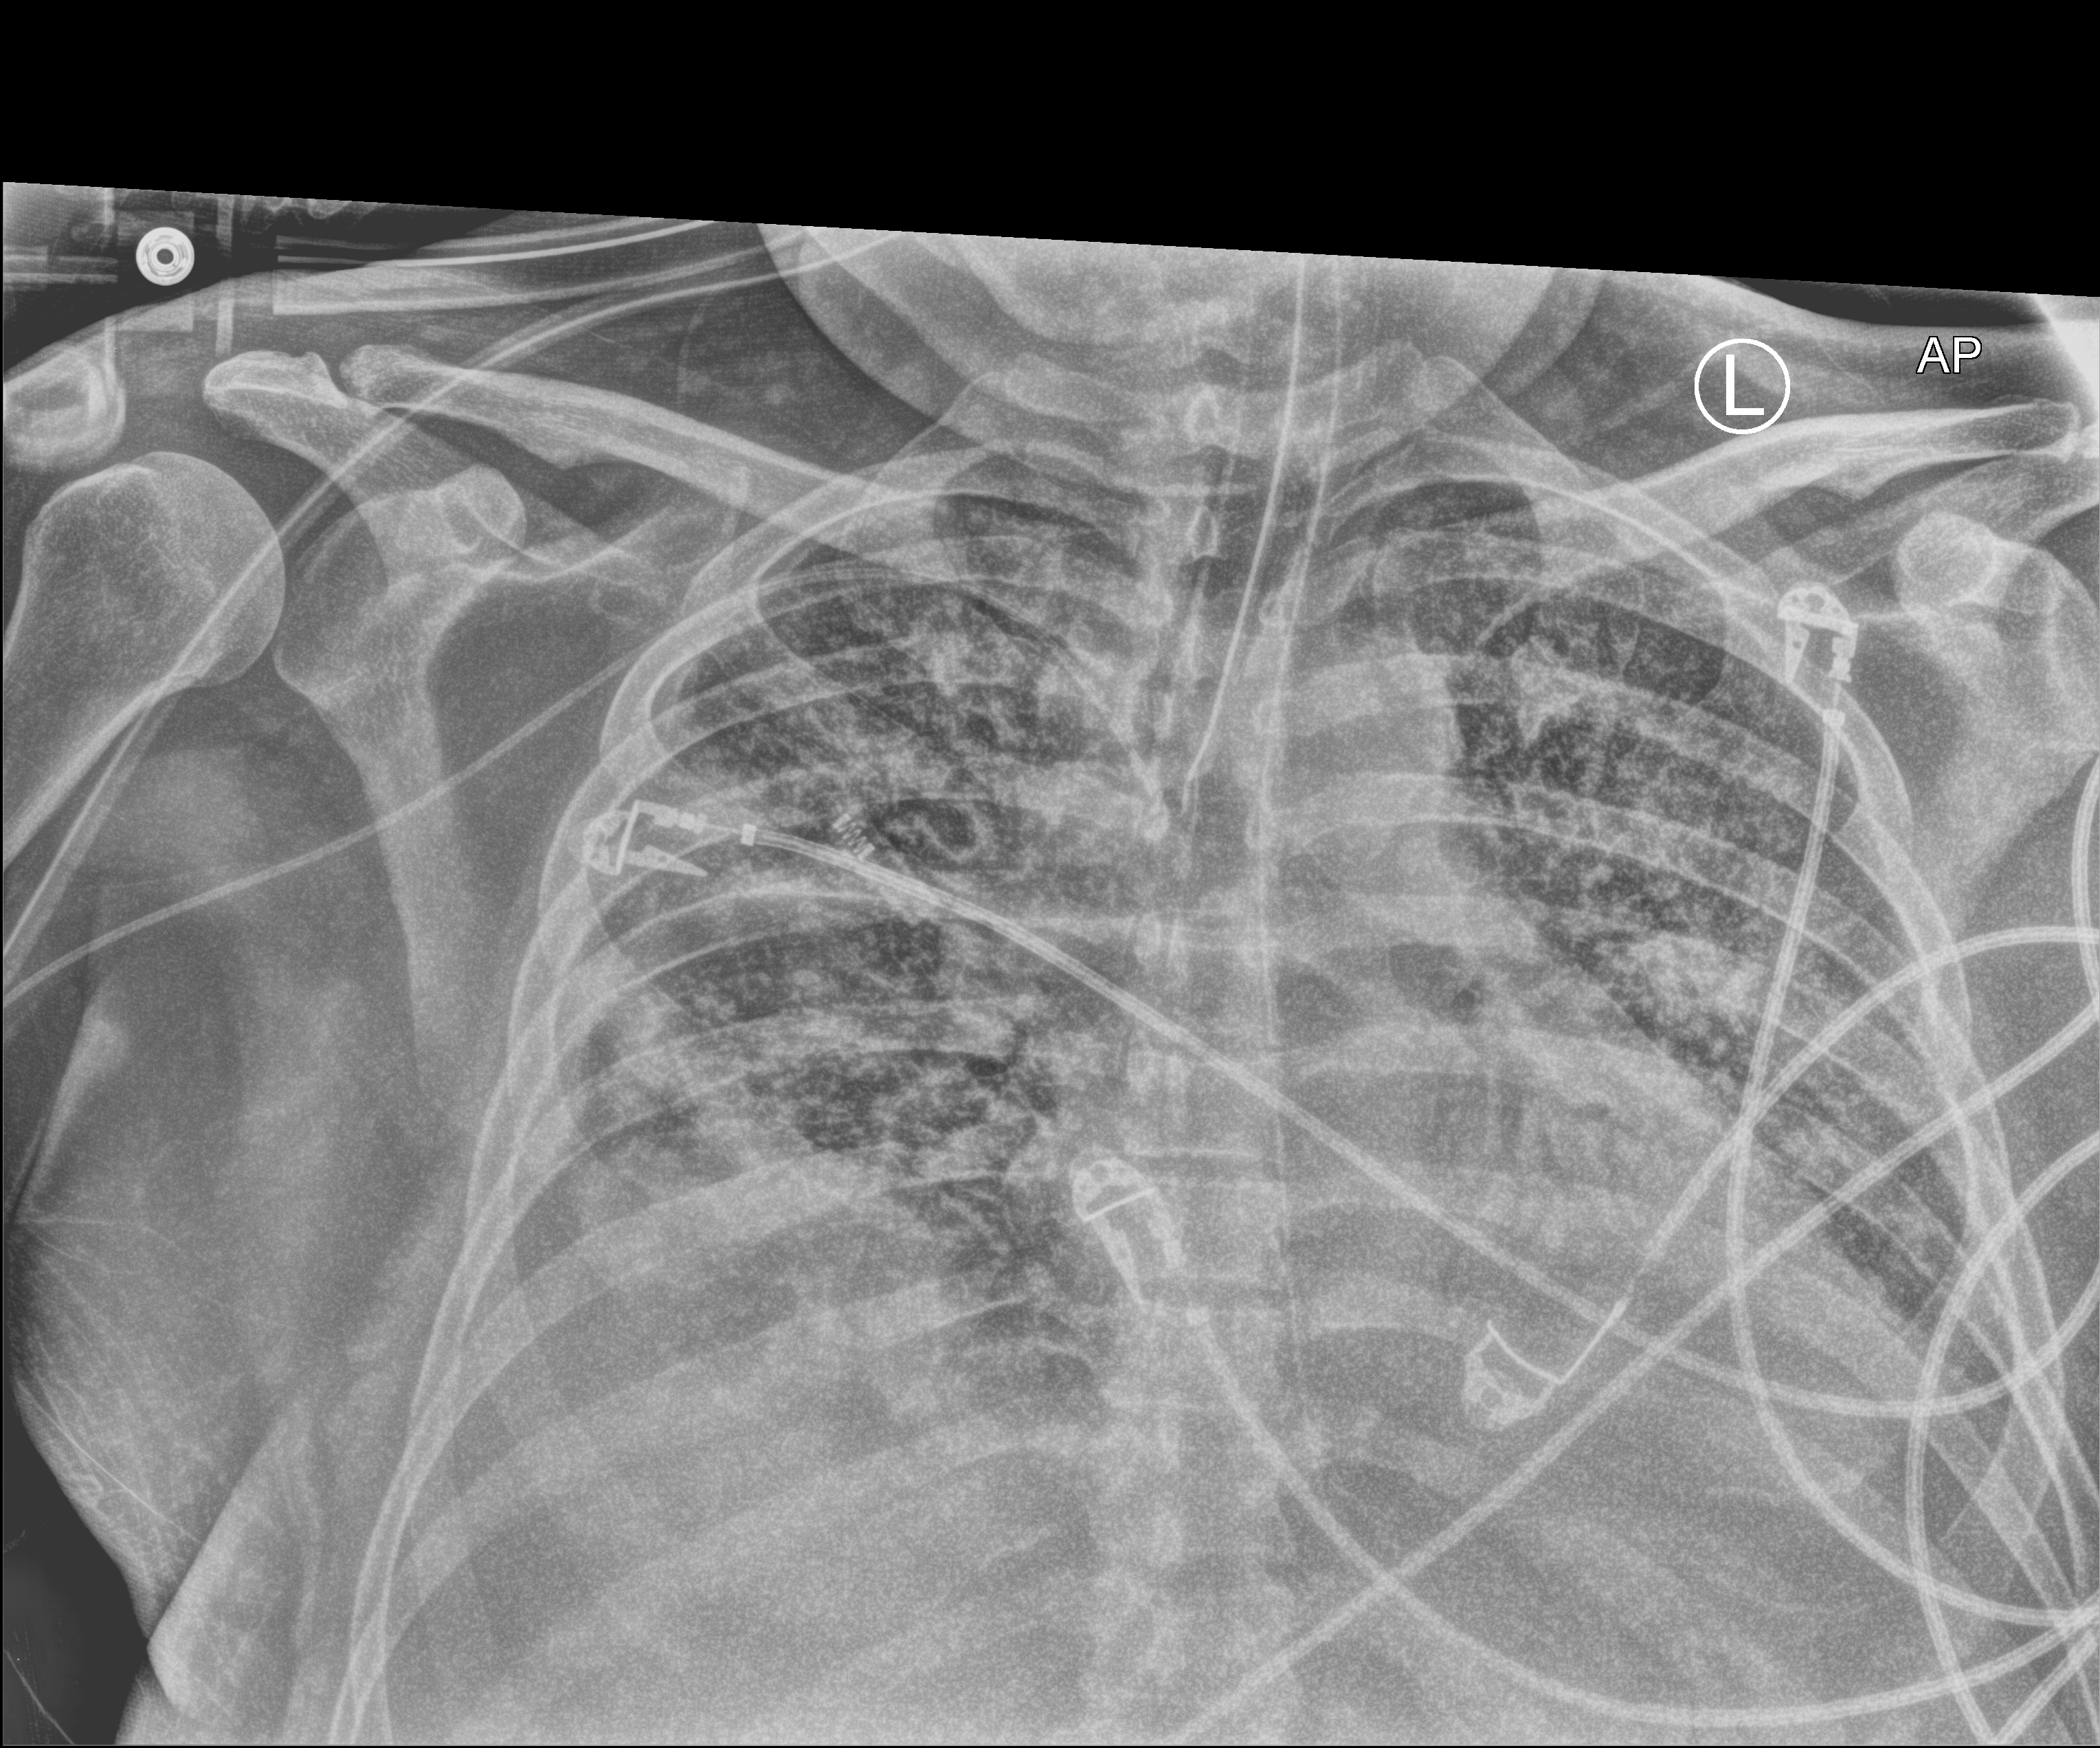
Bedside chest radiograph (computed radiography), anteroposterior (AP) projection. Male patient hospitalised with COVID-19, age 18–59 years.
Admission-level facts for this patient (not findings on this image; timing relative to this image not recorded): mechanically ventilated during this hospital stay: yes.